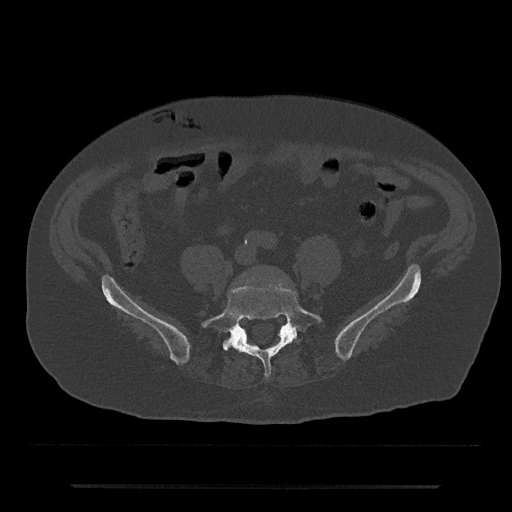
CT including the spine, one axial slice; slice 292 of 797 in the series (ordered by position); reconstruction kernel Br40s/3; 120 kVp; bone window (W 1800 / L 400 HU); 0.5 mm slice thickness; 512 × 512 image matrix, field of view 434 × 434 mm. Patient: male, 80 years. Case-level facts recorded for this patient, not image findings: primary cancer: prostate; vertebrae with lytic lesions (as recorded): L1, T11.
Structures marked on this image (semi-automatically segmented with operator editing):
- L5 vertebra: box from (x=202, y=286) to (x=322, y=378) px